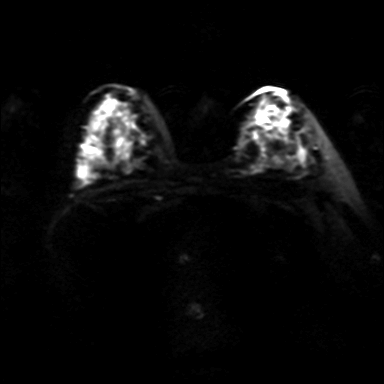
Breast MRI, one axial slice. Position 21 of 36 along the scan axis. Diffusion-weighted series; image 2 of 4 stored at this slice position (different b-values; order by instance number). 3 T. 4 mm slice thickness. 384 × 384 image matrix, field of view 320 × 320 mm. Female patient.
Annotated regions visible in this slice (expert manual segmentation):
- tumour on diffusion-weighted imaging: box from (x=249, y=107) to (x=287, y=140) px